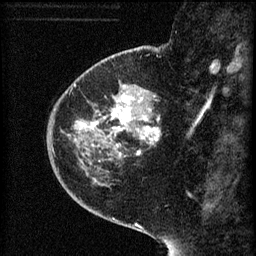
Breast MRI (dynamic contrast-enhanced), one sagittal slice; slice 19 of 60 in the series (ordered by position); 3 images stored at this slice position (order not interpretable as contrast timing); 1.5 T; TE 4.2 ms, TR 8.2 ms; 256 × 256 image matrix, field of view 180 × 180 mm. Patient: female, 44 years.
Outlined on this slice (semi-automatically segmented with operator editing):
- analysis volume of interest (the breast-tissue region the enhancement analysis was run in; not a lesion): bounding box (x1, y1, x2, y2) in pixels: (73, 82, 162, 165)
- tumour enhancement mask (voxels above the 70 % enhancement threshold inside the analysis volume of interest): (76, 86, 161, 159)